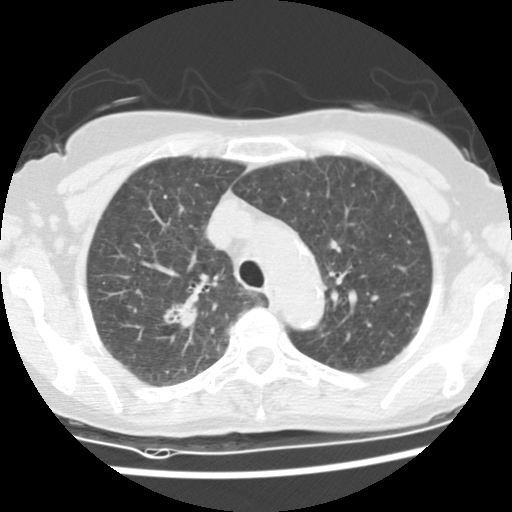
Low-dose screening chest CT, axial slice. First (baseline) screen. Lung window (W 1500 / L -600 HU). 2.5 mm slice thickness. Standard (soft-tissue) reconstruction kernel (STANDARD). 512 × 512 image matrix. Female, age 66 years at enrolment.
- Expert reader's lesion annotation, bounding box [x1, y1, x2, y2] px = [150, 292, 199, 336].
- Reader record for this screening exam (exam-level; its link to the box is not recorded): non-calcified nodule or mass ≥4 mm, right upper lobe, 13 × 11 mm, soft tissue attenuation.
- Later outcome: lung cancer diagnosed 64 days after this screen — adenocarcinoma, NOS, right upper lobe, poorly differentiated (G3), stage IA (AJCC 6th edition), 18 mm at pathology.